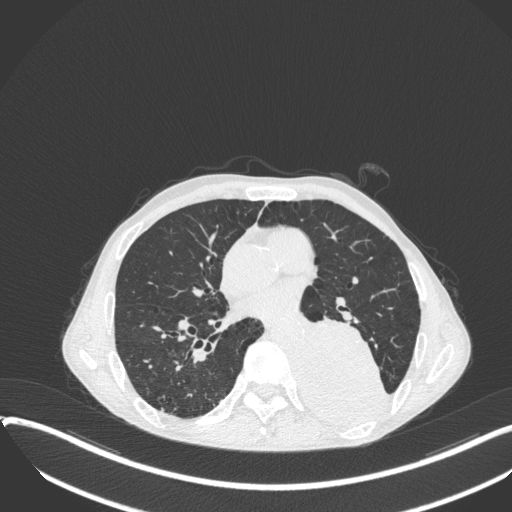
Chest CT, one axial slice; position 175 of 400 along the scan axis; reconstruction kernel B31f; lung window (W 1500 / L -600 HU); 1 mm slice thickness; 512 × 512 image matrix, field of view 400 × 400 mm. Male patient, age 57 years. Case-level facts recorded for this patient, not image findings: clinical TNM (as recorded): T4 N0 M0.
Outlined on this slice (rectangle marked by the reading radiologist):
- lung tumour (recorded histology: squamous cell carcinoma): box from (x=298, y=317) to (x=391, y=427) px